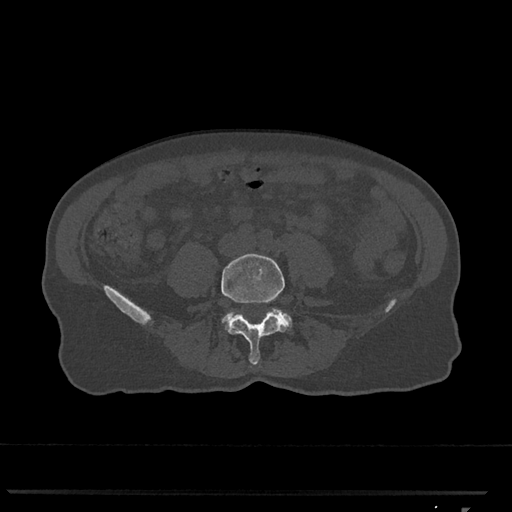
CT including the spine, one axial slice. Position 194 of 793 along the scan axis. Reconstruction kernel Br40s/3. Bone window (W 1800 / L 400 HU). 512 × 512 image matrix, field of view 380 × 380 mm. Female patient, age 62 years. From the clinical record (not read from this slice): primary cancer: renal.
Outlined on this slice (semi-automatically segmented with operator editing):
- L4 vertebra: box from (x=221, y=253) to (x=287, y=365) px
- L5 vertebra: (x=223, y=310)–(x=292, y=328)